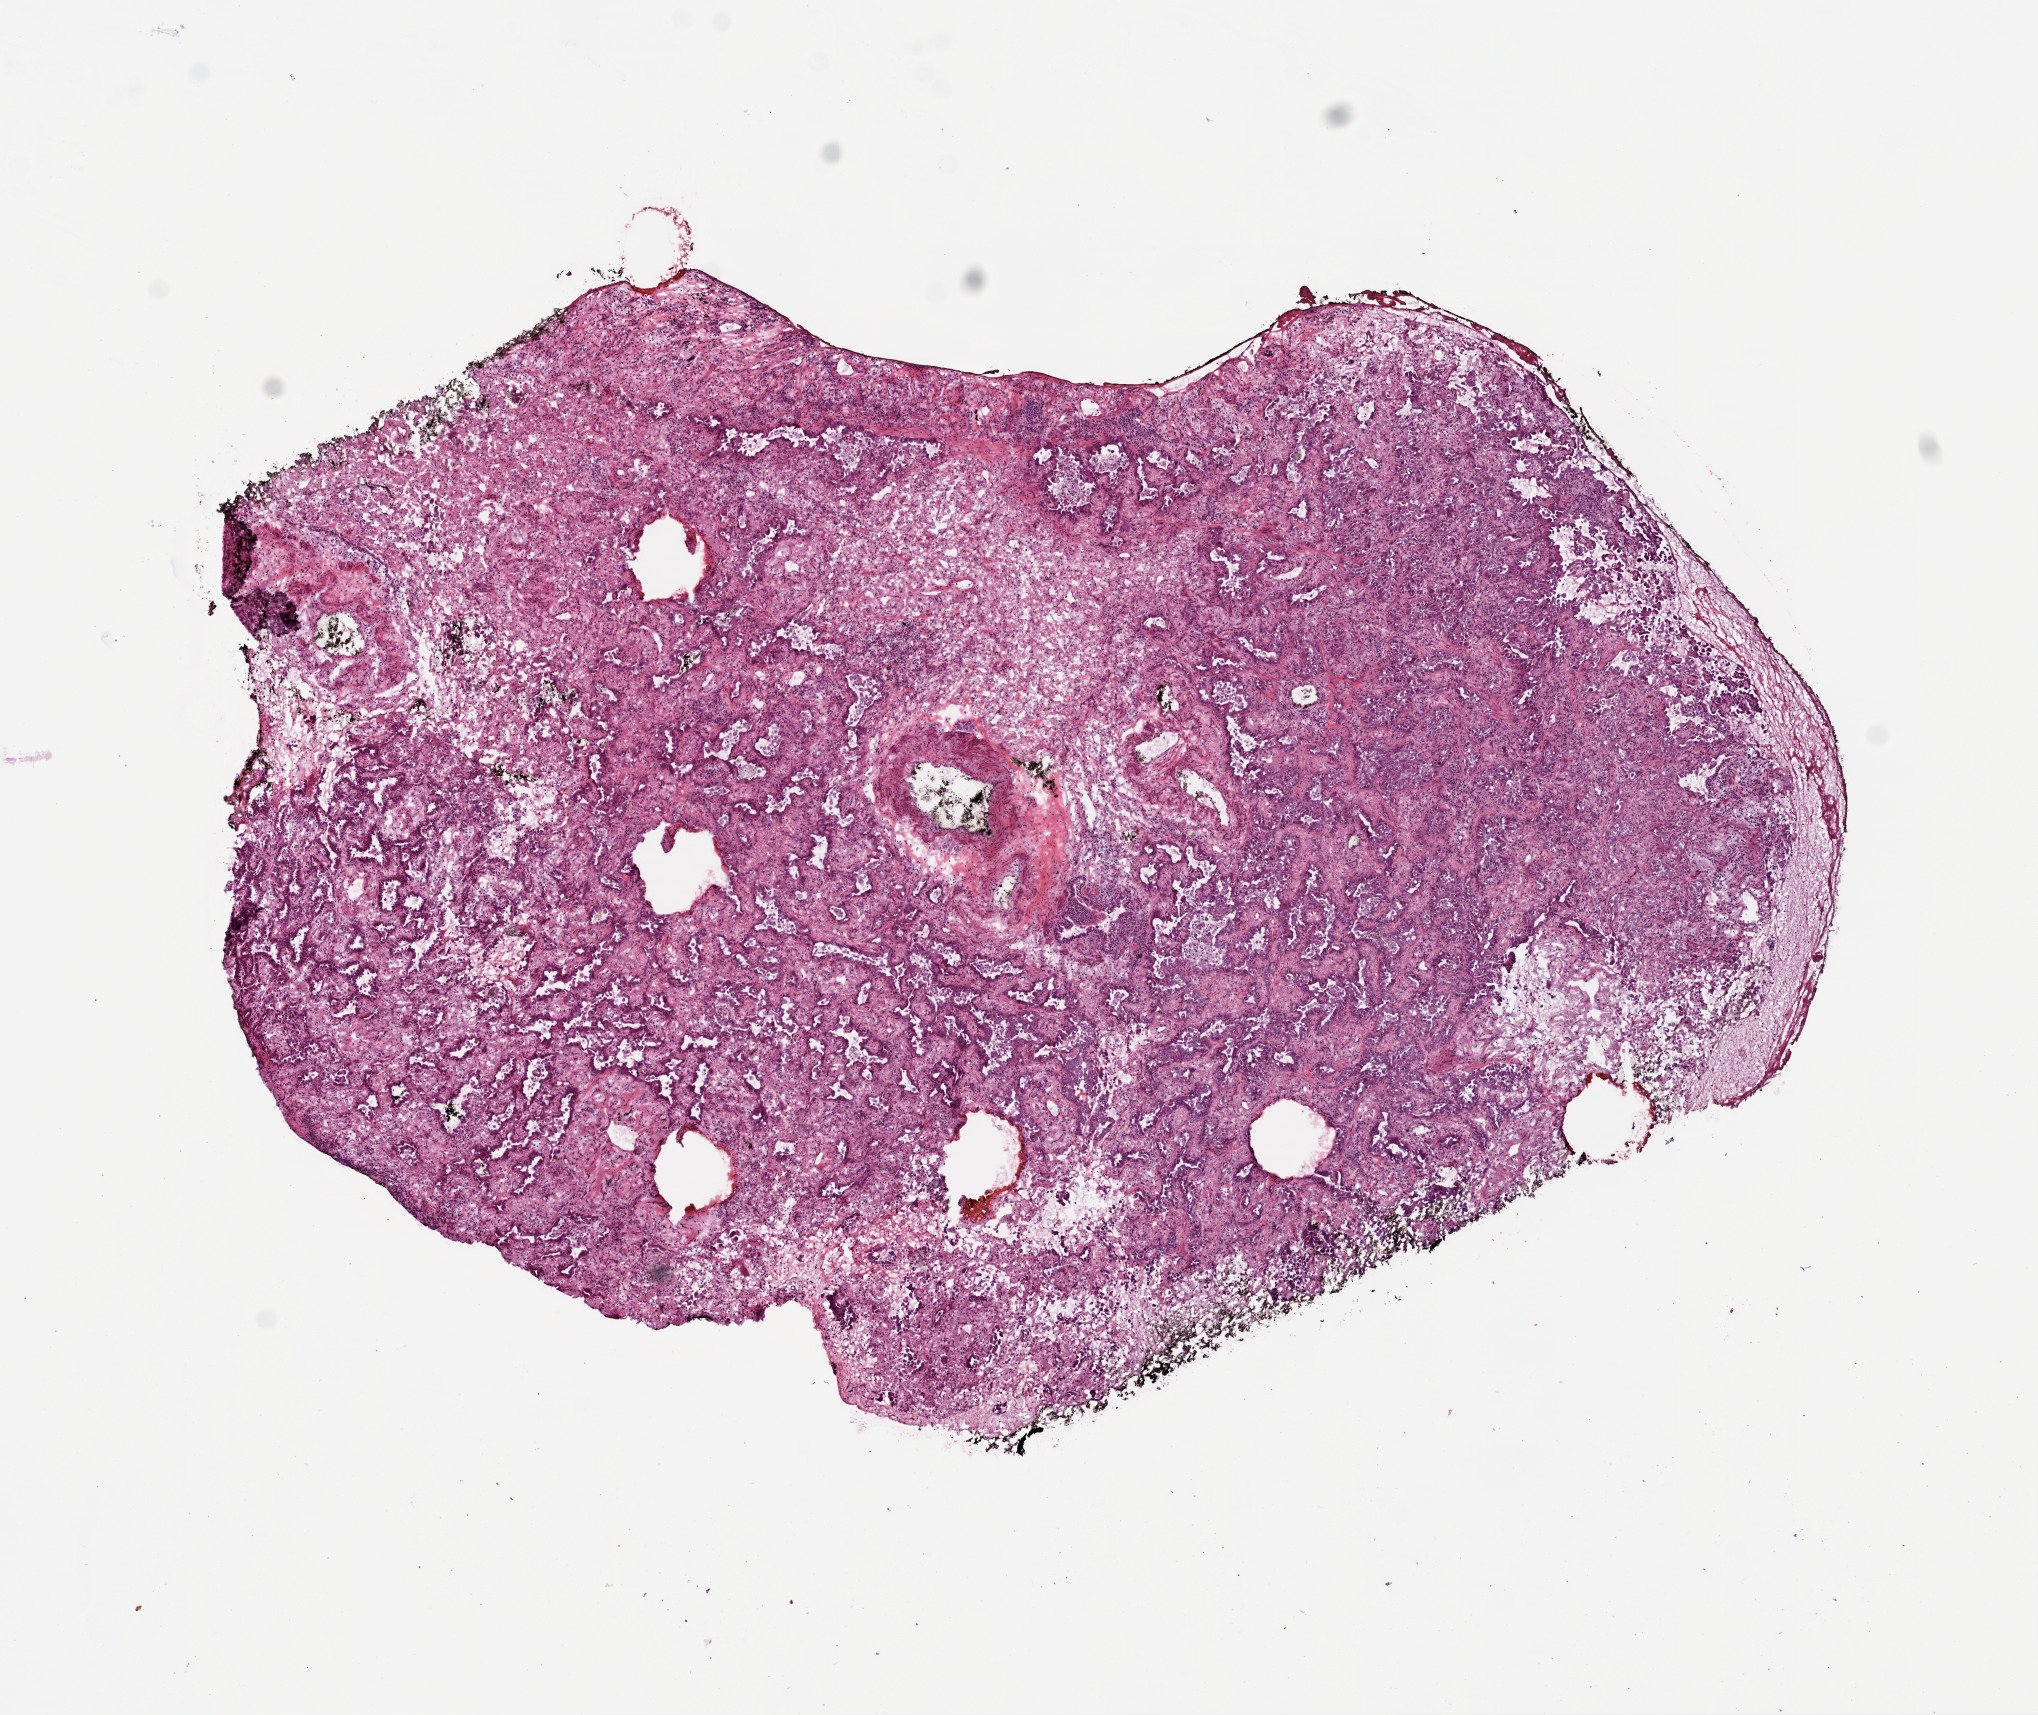
Whole-slide histology image, H&E, low-resolution overview of the scanned area, about 8.2 x 6.9 mm. Frozen section from the top of the tissue portion. Lung, primary tumour sample. Patient: male, age at initial diagnosis 56 years. Pathologist review of this section (percent, as recorded): tumour cells 60%, tumour nuclei 60%, normal cells 0%, stromal cells 40%, necrosis 0%.
Pathologic diagnosis: Bronchiolo-alveolar carcinoma, non-mucinous (lower lobe, lung). AJCC pathologic stage: IA (6th edition). TNM: T1 N0 M0. Laterality: right.